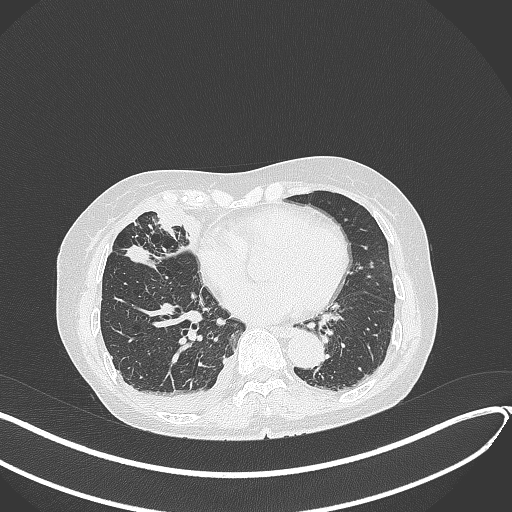
Chest CT, one axial slice; slice 152 of 418 in the series (ordered by position); reconstruction kernel B70f; 120 kVp; lung window (W 1500 / L -600 HU); 1 mm slice thickness; 512 × 512 image matrix, field of view 400 × 400 mm. Patient: female, 75 years. Case-level facts recorded for this patient, not image findings: clinical TNM (as recorded): T2a N3 M0.
Annotated regions visible in this slice (bounding box drawn by a radiologist):
- lung tumour (recorded histology: adenocarcinoma): bounding box (x1, y1, x2, y2) in pixels: (123, 244, 153, 267)